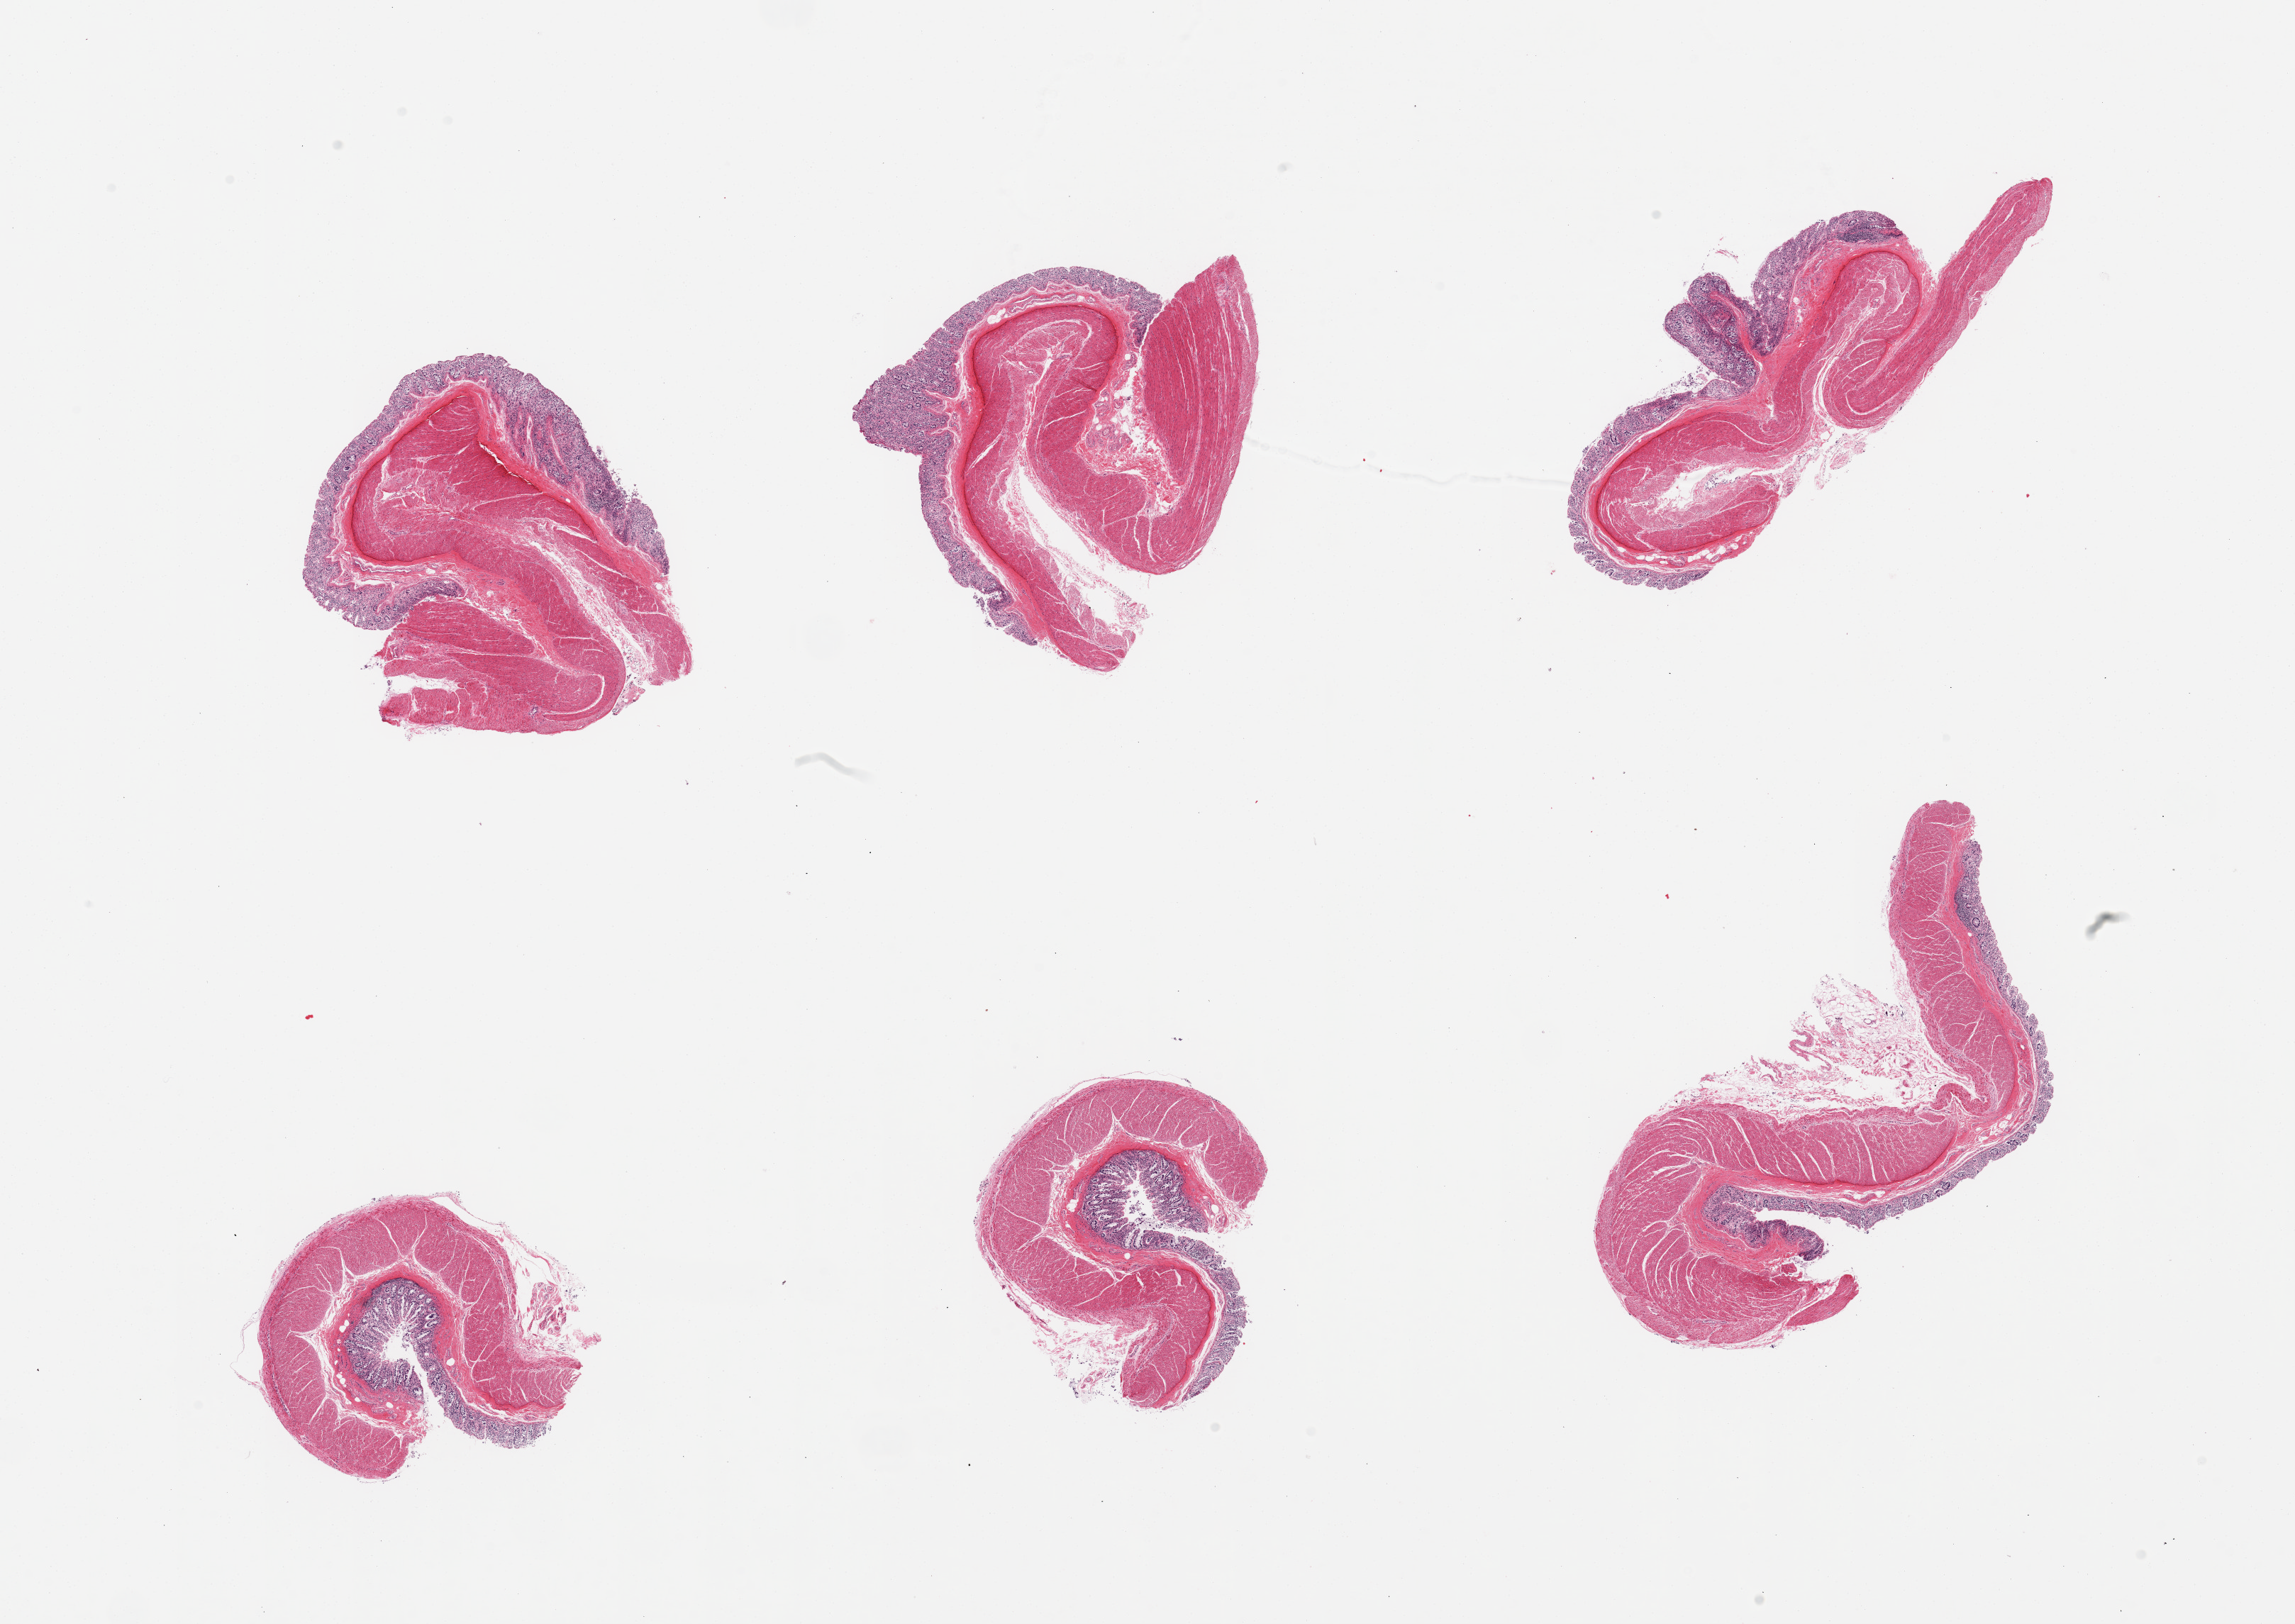
Whole-slide image, hematoxylin and eosin (H&E) stain, brightfield, a low-resolution overview of the entire scanned area, about 25.6 x 18.1 mm; PAXgene-fixed paraffin-embedded (PFPE) section; target tissue: transverse colon; donor tissue sample.
- reviewer comment on this tissue sample: 6 pieces, mucosa up to ~0.5mm but glandular epithelium totally autolyzed, residual lamina propria remains